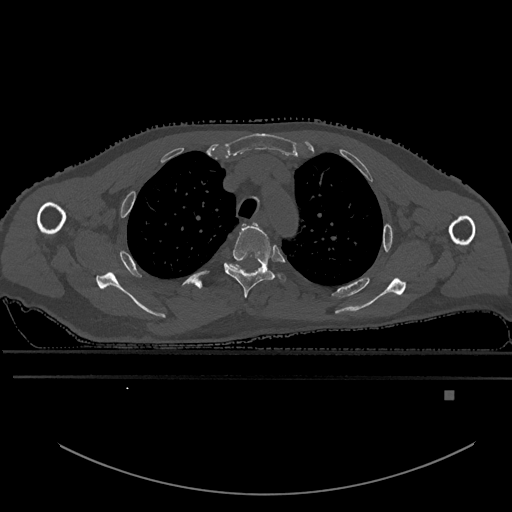
CT including the spine, one axial slice; position 448 of 969 along the scan axis; bone window (W 1800 / L 400 HU); 0.5 mm slice thickness; 512 × 512 image matrix, field of view 456 × 456 mm. Male patient, age 82 years. Case-level facts recorded for this patient, not image findings: primary cancer: prostate; vertebrae with lytic lesions (as recorded): T11, T9, T8, T2.
Structures marked on this image (semi-automatic segmentation, software-assisted and operator-edited):
- T3 vertebra: box from (x=224, y=223) to (x=286, y=298) px
- T4 vertebra: (x=226, y=263)–(x=239, y=268)